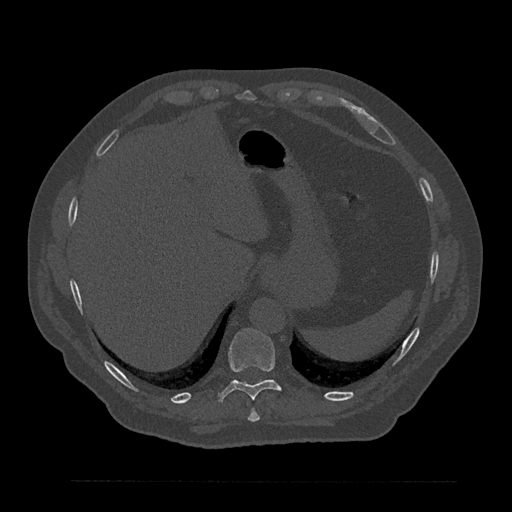
CT including the spine, one axial slice; position 346 of 797 along the scan axis; reconstruction kernel Br40s/3; 120 kVp; bone window (W 1800 / L 400 HU); 512 × 512 image matrix, field of view 430 × 430 mm. Patient: male, 61 years. From the clinical record (not read from this slice): primary cancer: prostate.
Structures marked on this image (semi-automatically segmented with operator editing):
- T10 vertebra: bounding box [x1, y1, x2, y2] px = [217, 329, 282, 402]
- T9 vertebra: [247, 408, 260, 422]